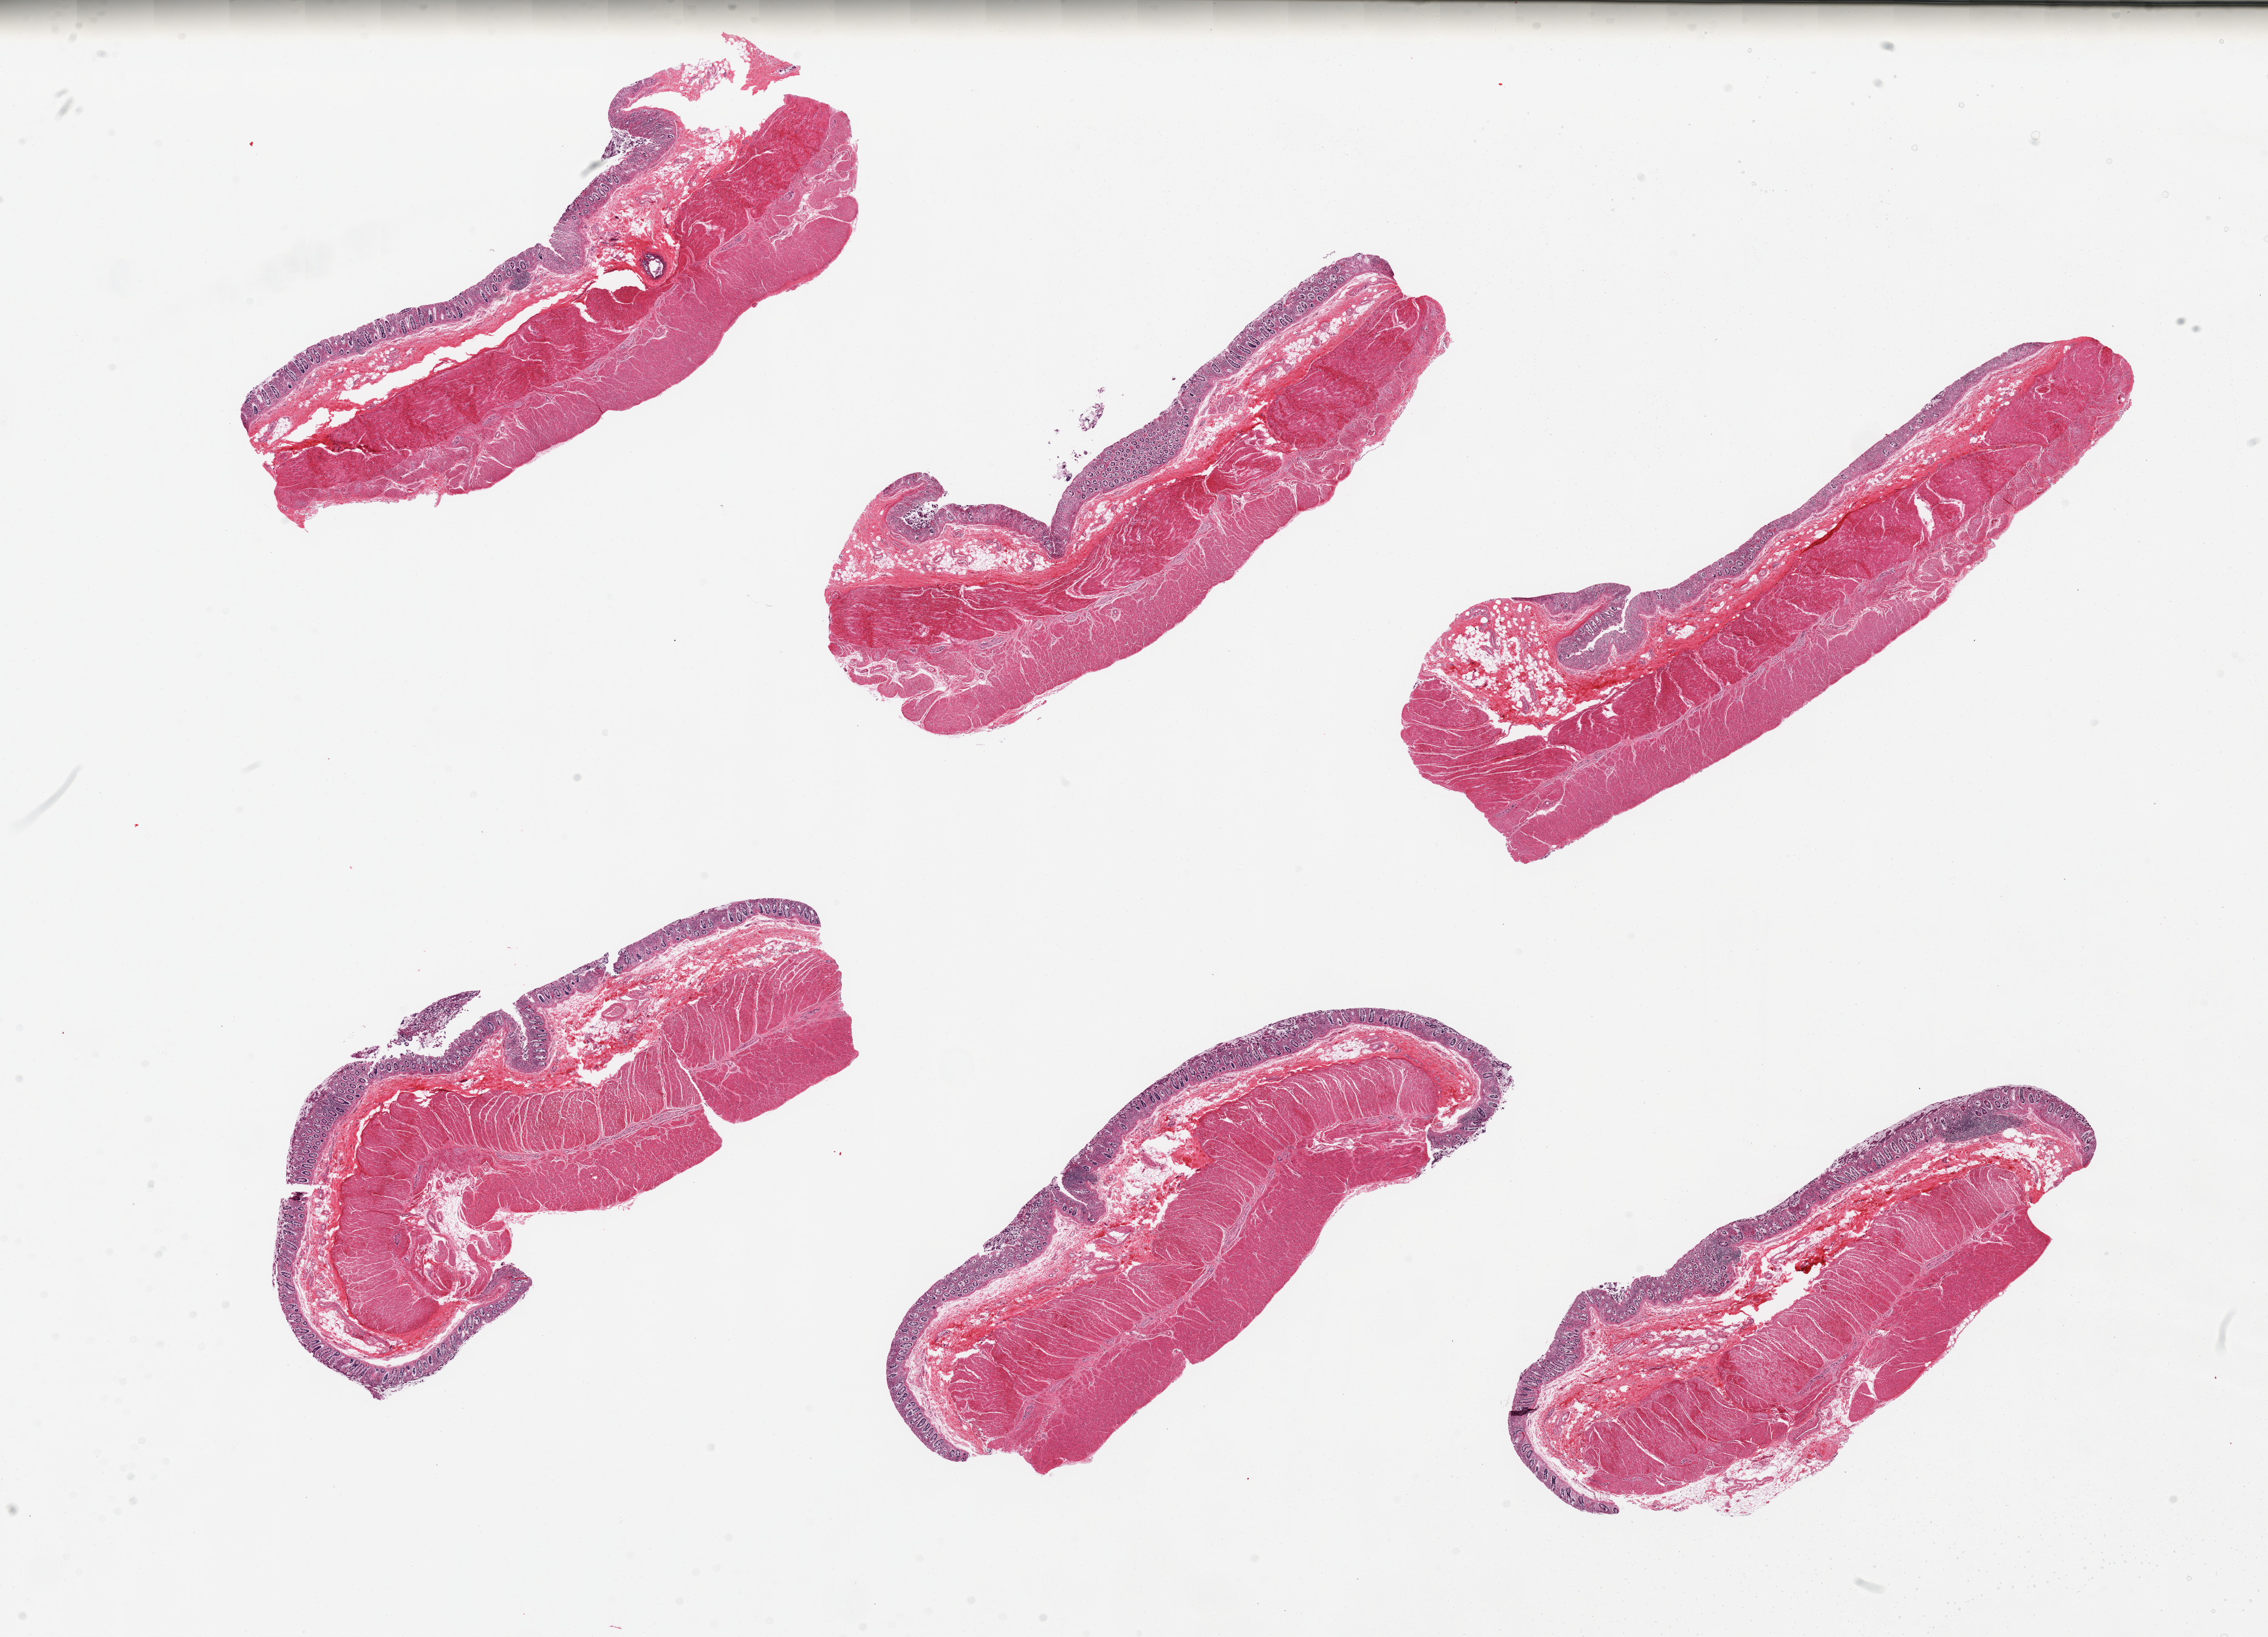
Digitized hematoxylin and eosin (H&E)-stained section, whole scanned area (about 29.5 x 21.3 mm) shown as a low-resolution overview; PAXgene-fixed, paraffin-embedded tissue; sampled site (target tissue): transverse colon; tissue donor sample. Donor sex: male.
* review note (as recorded): 6 pieces, mucosa is ~0.3mm thick, moderately-severely autolyzed